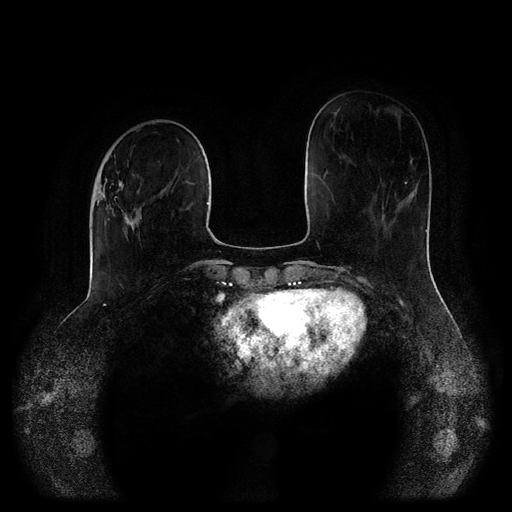
Breast MRI (dynamic contrast-enhanced, multi-phase), one axial slice; position 33 of 116 along the scan axis; dynamic contrast-enhanced series, time point 2 of 5 at this slice position (early post-contrast); 1.5 T; TE 2.6 ms, TR 5.2 ms; 2 mm slice thickness; 512 × 512 image matrix. Patient: female, 52 years.
Outlined on this slice (semi-automatically segmented with operator editing):
- breast lesion (labelled 'tumour' in the annotation; benign lesions carry a separate 'benign' label): bounding box <97,171,142,234> (left, top, right, bottom; pixels)